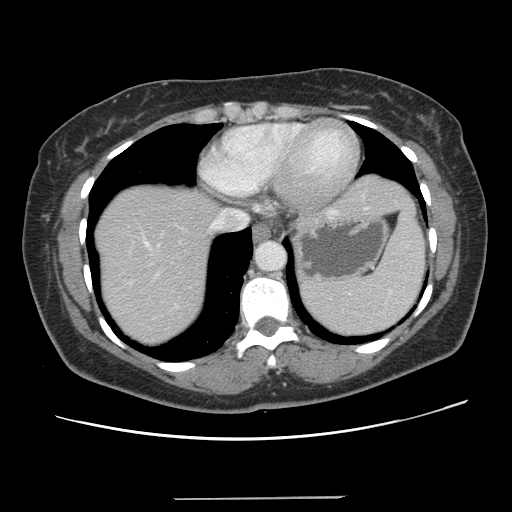
Contrast-enhanced abdominal CT, one axial slice. Position 118 of 141 along the scan axis. Soft-tissue window (W 400 / L 40 HU). 2.5 mm slice thickness. 512 × 512 image matrix. Female patient, age 53 years. From the clinical record (not read from this slice): diagnosis: colorectal cancer liver metastases, imaged before liver resection; multiple liver metastases: no; largest metastasis: 14.5 cm; disease in both lobes: yes.
Outlined on this slice (manually delineated by an expert):
- hepatic veins: bounding box (x1, y1, x2, y2) in pixels: (118, 210, 246, 278)
- liver: (95, 175, 410, 346)
- planned liver remnant (the part of the liver to remain after resection): (94, 213, 215, 345)